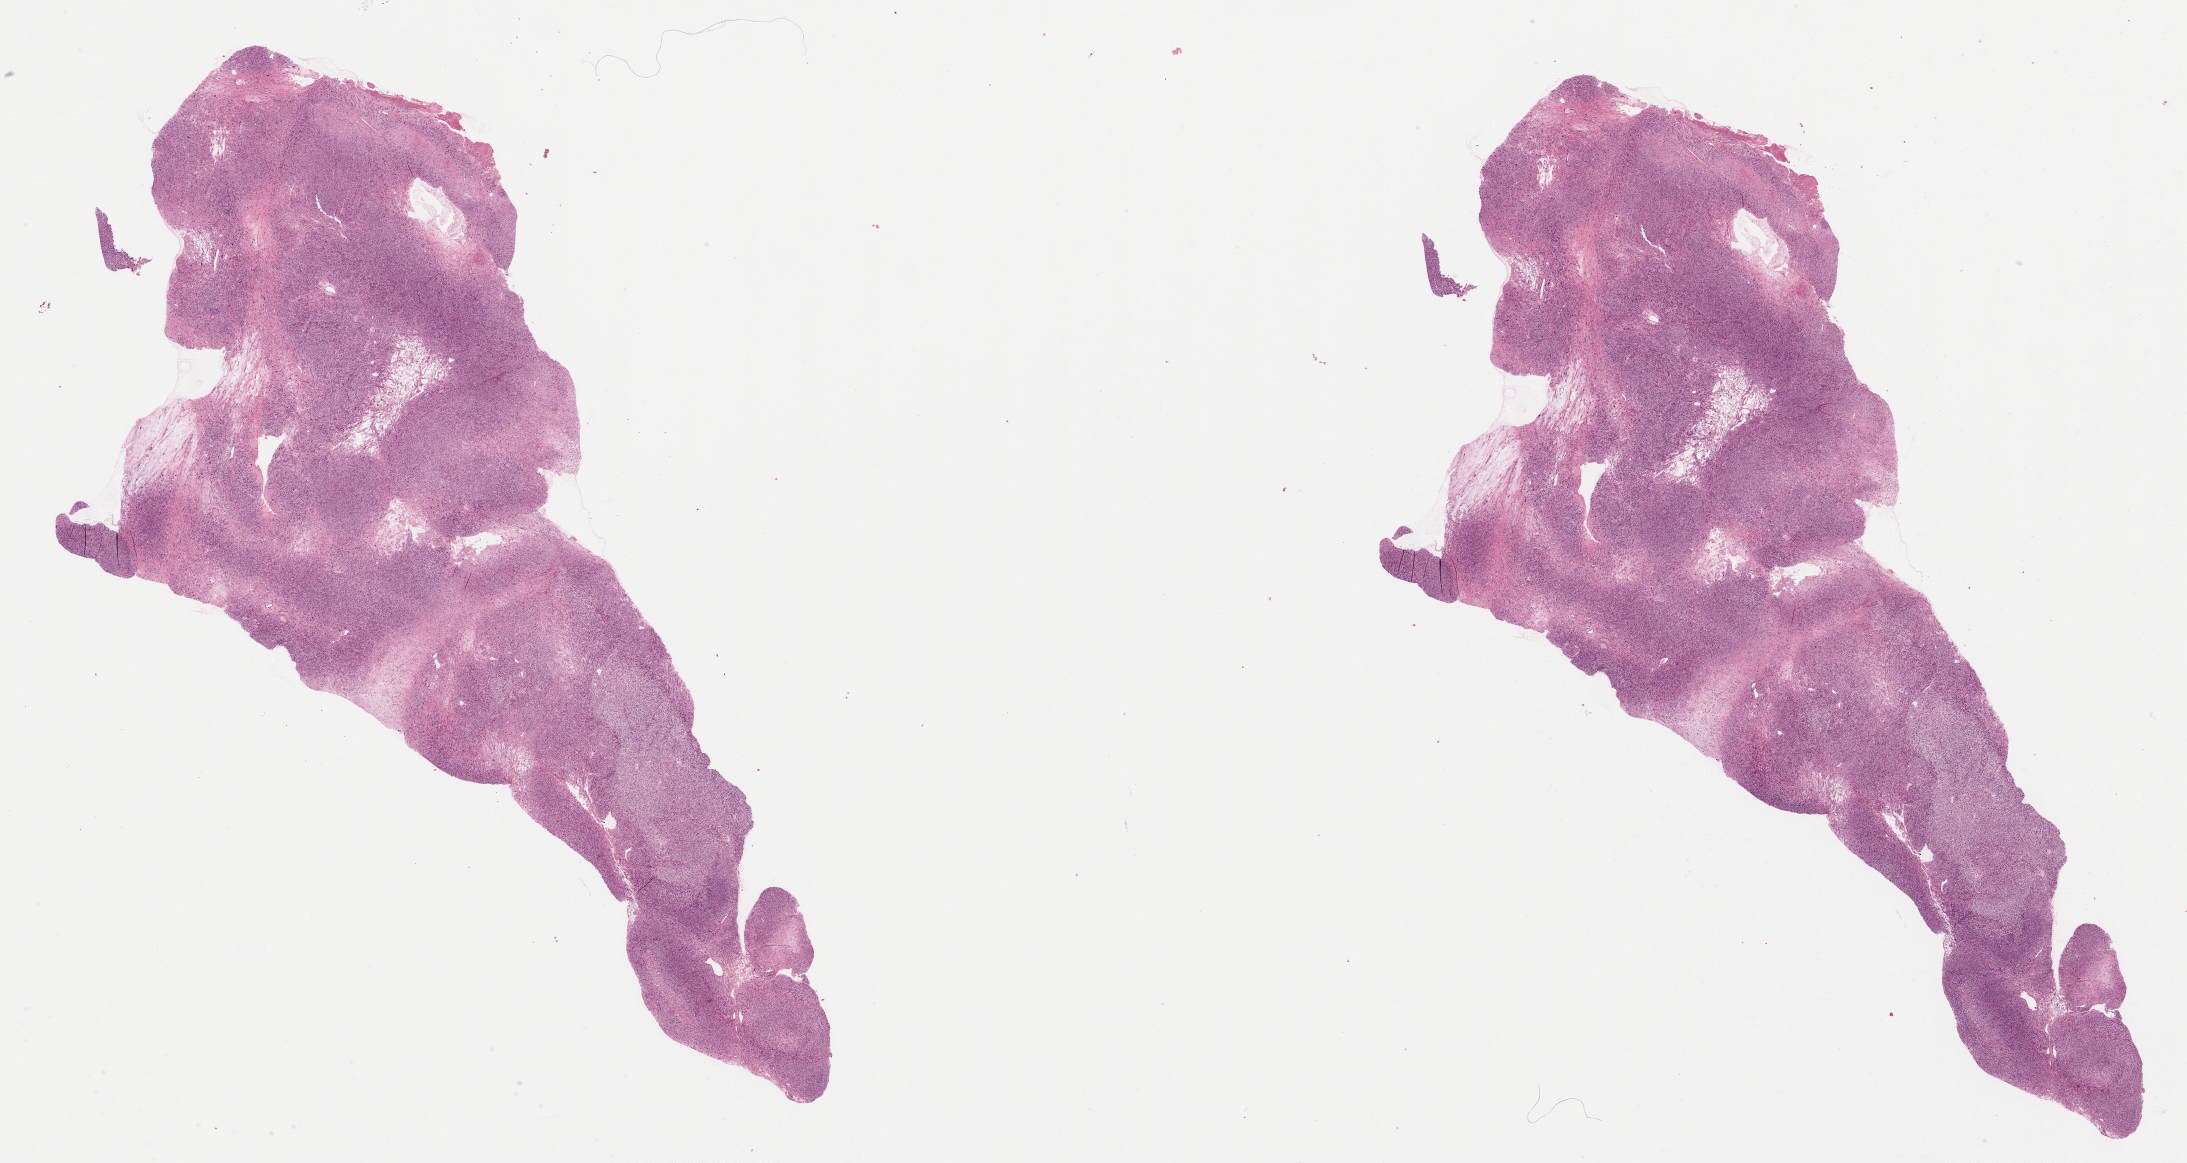
Hematoxylin and eosin (H&E) stained whole-slide image — shown as a low-resolution overview of the whole scanned area (about 35.0 x 18.6 mm, slide scanned at 20x); FFPE section; retroperitoneum and peritoneum, primary tumour sample. Female patient; age at initial diagnosis 67 years.
Pathologic diagnosis: Leiomyosarcoma, NOS (retroperitoneum).